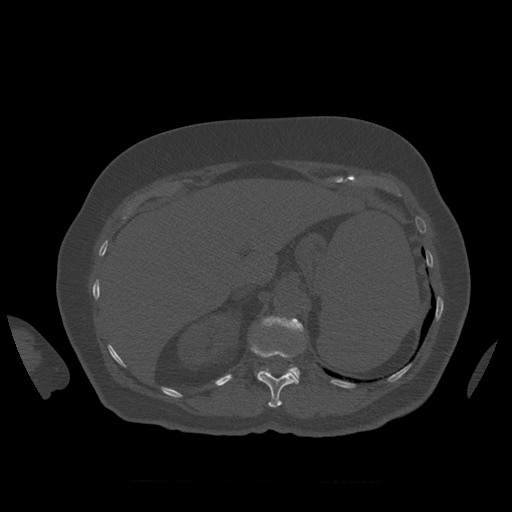
CT including the spine, one axial slice. Slice 294 of 399 in the series (ordered by position). 120 kVp. Bone window (W 1800 / L 400 HU). 1.25 mm slice thickness. 512 × 512 image matrix. Patient age 81 years. Case-level facts recorded for this patient, not image findings: primary cancer: renal.
Structures marked on this image (semi-automatic segmentation, software-assisted and operator-edited):
- L1 vertebra: bounding box <259,317,304,382> (left, top, right, bottom; pixels)
- T12 vertebra: <251,343,299,408>